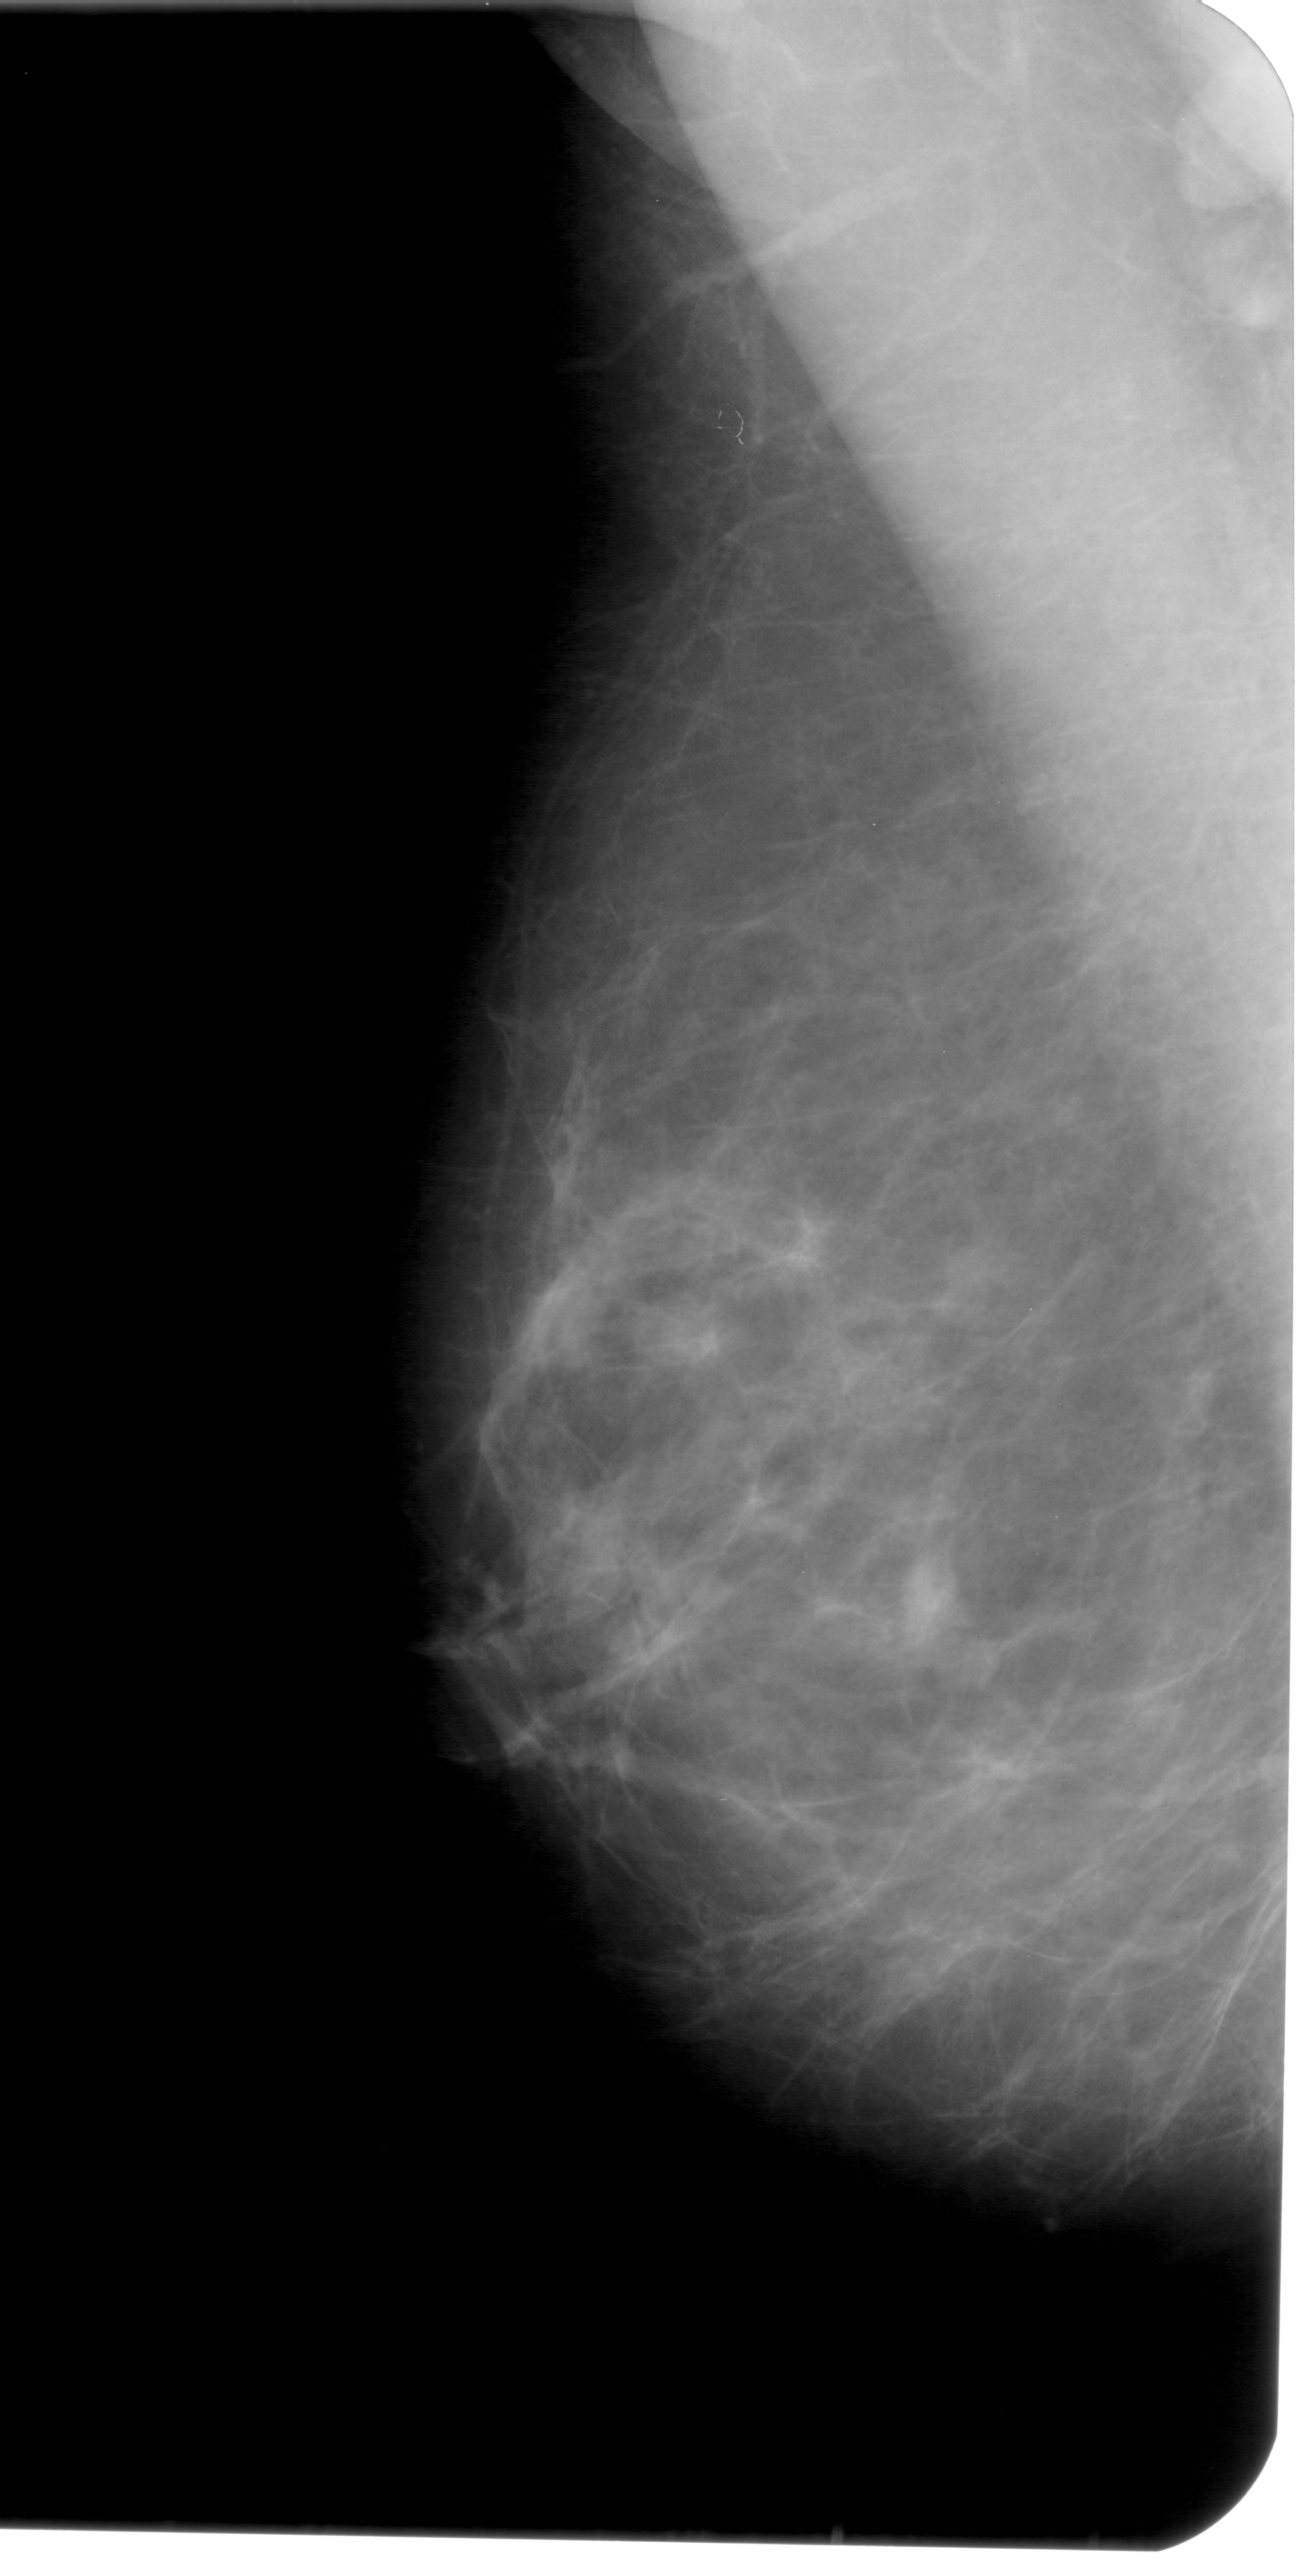
Scanned film-screen mammogram; left breast; mediolateral oblique (MLO) view; breast composition: scattered fibroglandular densities (BI-RADS density category 2 of 4).
Abnormality record for this image: mass, shape irregular, margins ill defined; BI-RADS assessment category 4; subtlety rating 3 on a 1 (subtle) to 5 (obvious) scale; pathology result (as recorded, not read from the image): benign.